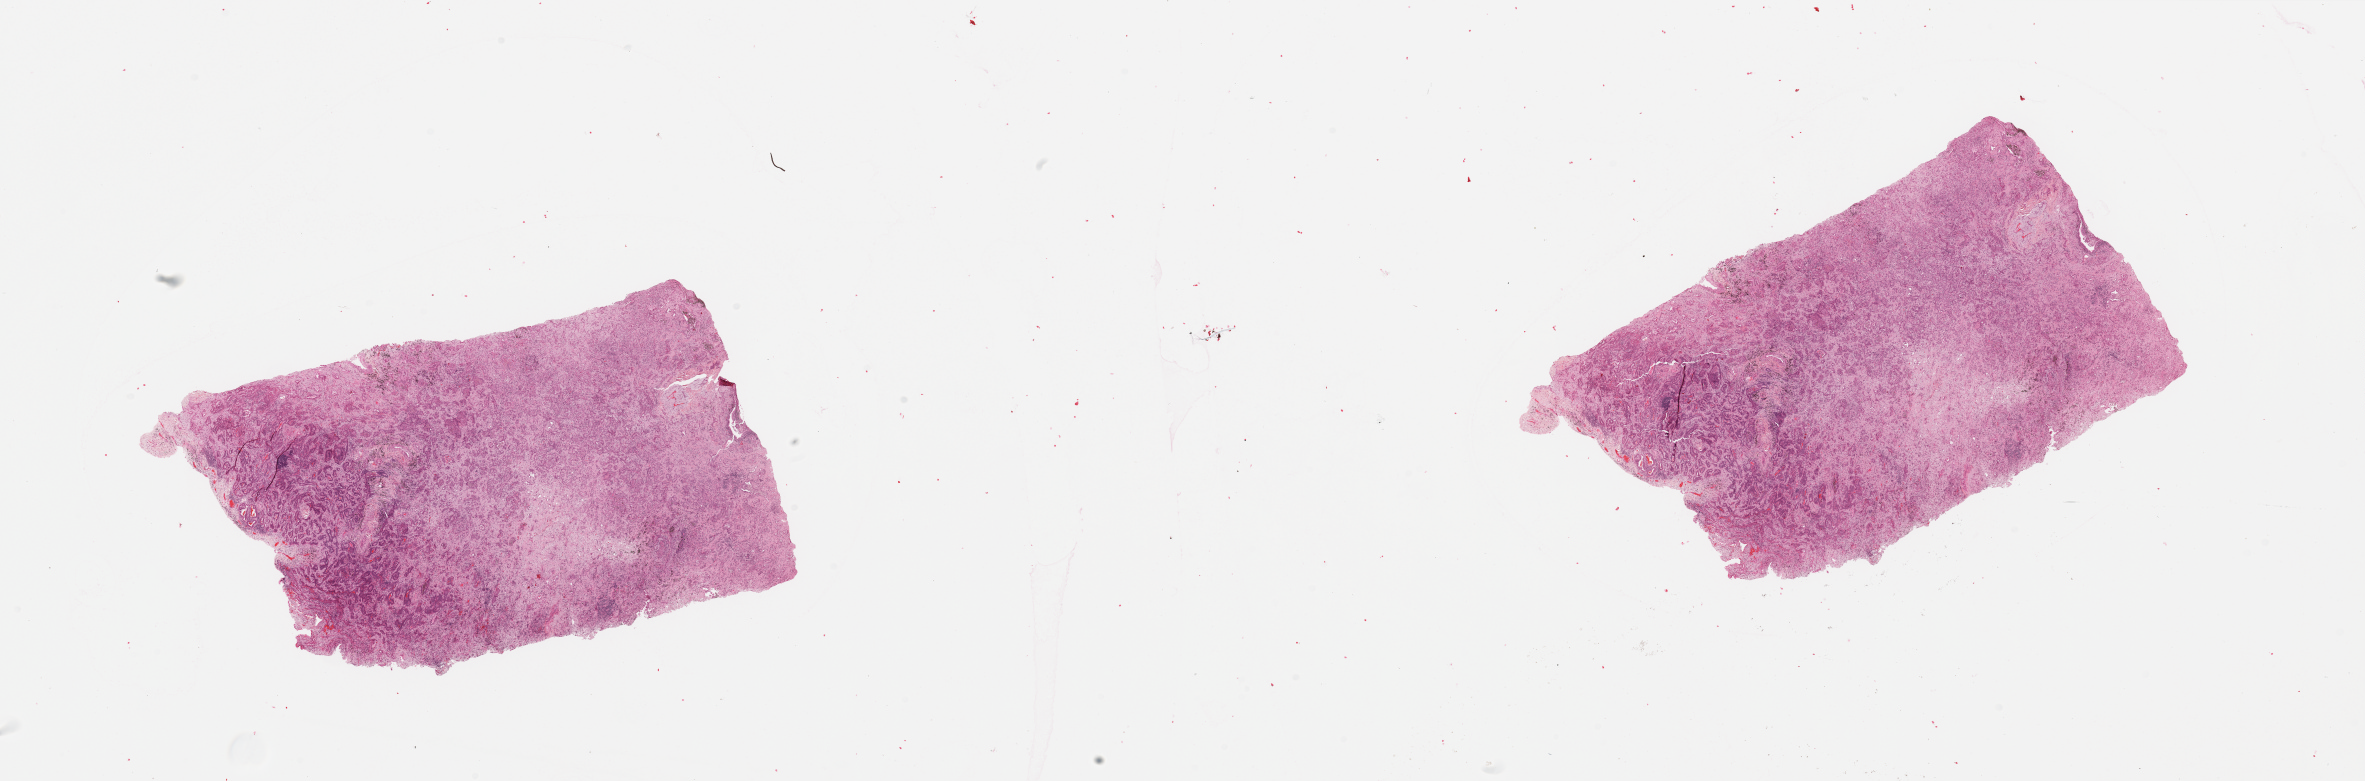
H&E-stained whole-slide image, whole scanned area (about 37.4 x 12.4 mm) shown as a low-resolution overview, lung, tumour tissue. 69-year-old female patient. Histologic grade: G2 (moderately differentiated).
AJCC pathologic stage: IB. Primary tumour site (as recorded): right upper lobe. Histologic diagnosis: Adenocarcinoma, NOS.